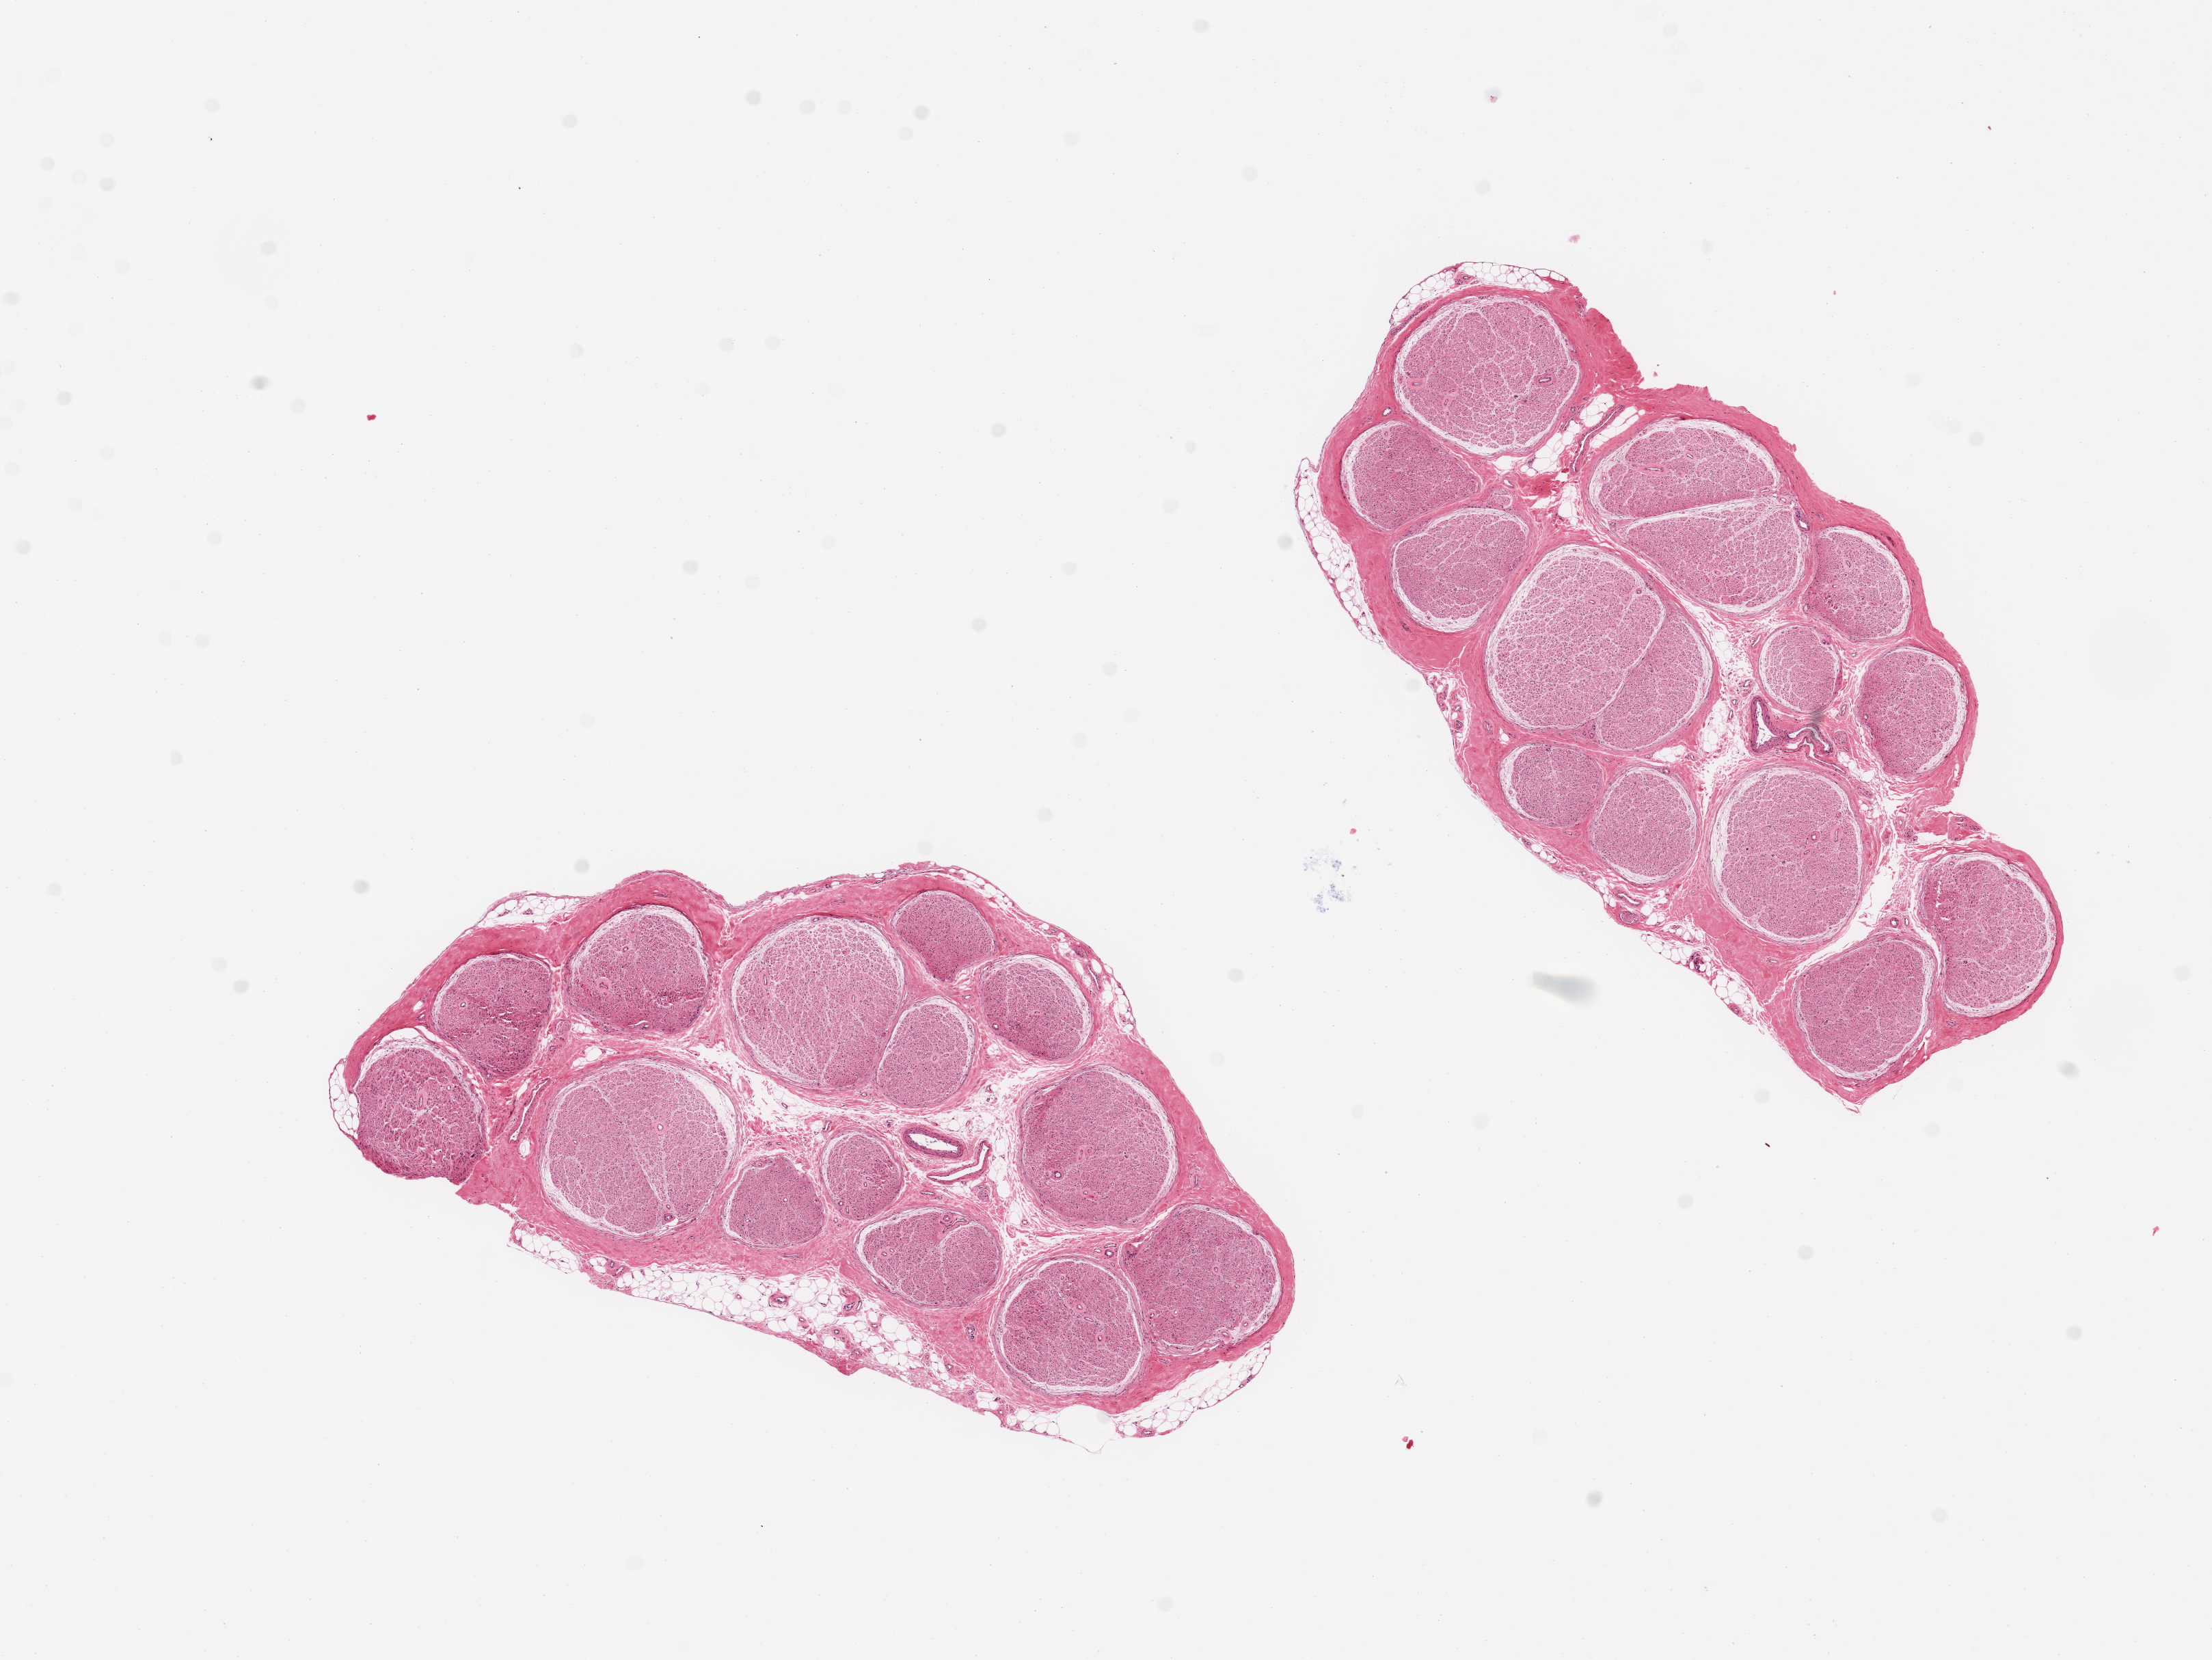
Whole-slide image, H&E stain, brightfield, low-resolution overview of the scanned area, about 12.8 x 9.6 mm (from a 20x scan), PAXgene-fixed, paraffin-embedded tissue, section of tibial nerve (target tissue), tissue donor sample. Donor sex: male.
* pathologist's review note for this sample: 2 pieces; trace adherent fat